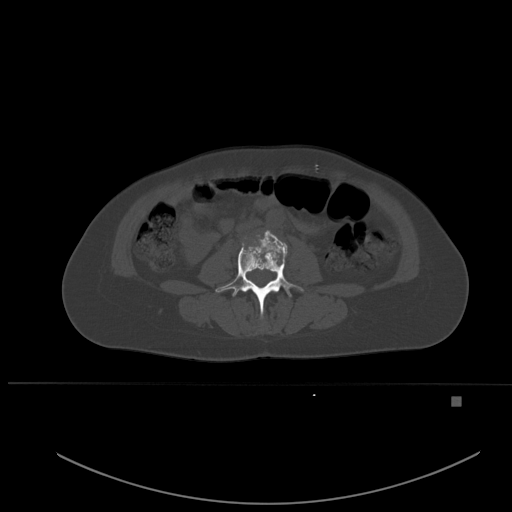
CT including the spine, one axial slice. Slice 193 of 651 in the series (ordered by position). Bone window (W 1800 / L 400 HU). 1.5 mm slice thickness. 512 × 512 image matrix, field of view 443 × 443 mm. Female patient, age 49 years. Case-level facts recorded for this patient, not image findings: primary cancer: breast; vertebrae with lytic lesions (as recorded): L3, T12, L4.
Outlined on this slice (semi-automatic segmentation, software-assisted and operator-edited):
- L3 vertebra: box from (x=216, y=231) to (x=304, y=316) px